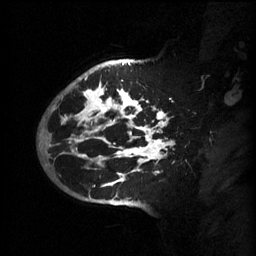
Breast MRI (dynamic contrast-enhanced), one sagittal slice. Slice 44 of 60 in the series (ordered by position). 3 images stored at this slice position (order not interpretable as contrast timing). 1.5 T. TE 4.2 ms, TR 11 ms. 2 mm slice thickness. 256 × 256 image matrix, field of view 220 × 220 mm. Female patient, age 51 years.
Structures marked on this image (semi-automatically segmented with operator editing):
- analysis volume of interest (the breast-tissue region the enhancement analysis was run in; not a lesion): box from (x=63, y=80) to (x=176, y=201) px
- tumour enhancement mask (voxels above the 70 % enhancement threshold inside the analysis volume of interest): (x=63, y=80)–(x=174, y=187)